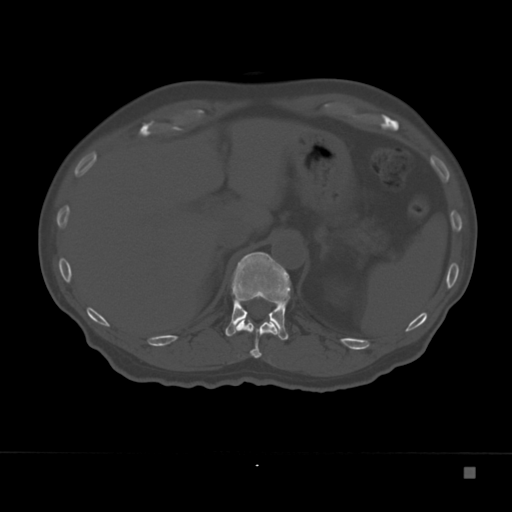
CT including the spine, one axial slice. Slice 141 of 332 in the series (ordered by position). 120 kVp. Bone window (W 1800 / L 400 HU). 512 × 512 image matrix. Patient: male, 72 years. Case-level facts recorded for this patient, not image findings: primary cancer: skeletal.
Structures marked on this image (semi-automatic segmentation, software-assisted and operator-edited):
- T11 vertebra: box from (x=234, y=318) to (x=281, y=358) px
- T12 vertebra: (x=225, y=252)–(x=291, y=340)